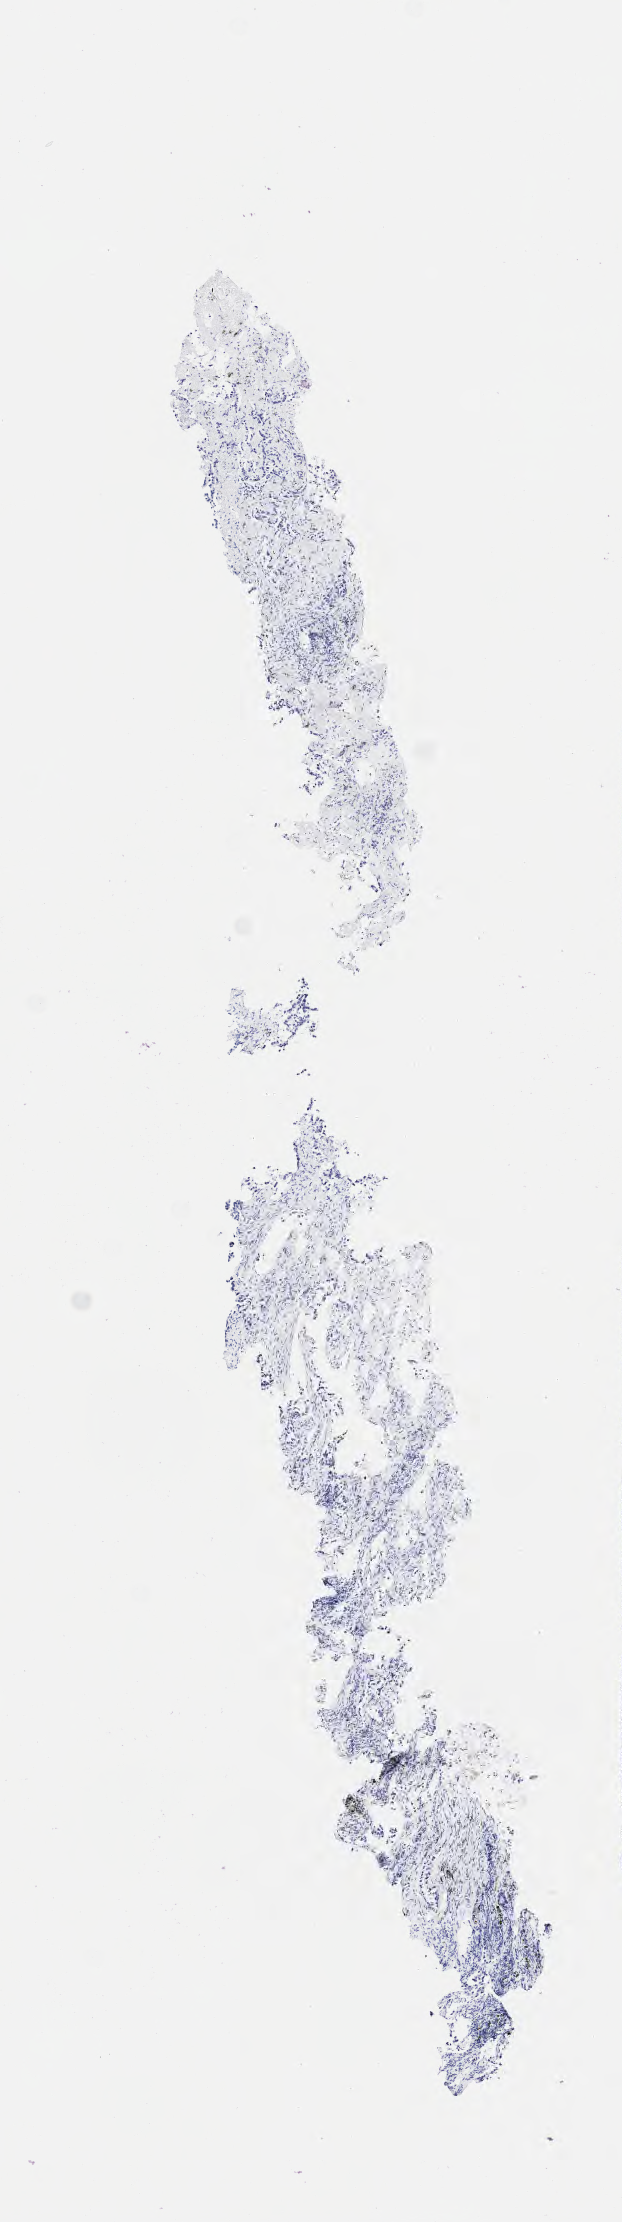
IHC for p40, whole-slide image, a low-resolution overview of the entire scanned area, about 2.5 x 9.0 mm; specimen: tumor tissue; anatomic site: lung. Patient: male, 67 years old.
Diagnosis: Adenocarcinoma, NOS.